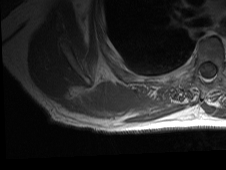
MRI of an extremity soft-tissue mass, one axial slice; MR volume resampled by the dataset authors to the PET/CT grid (not the native acquisition matrix); 226 × 170 image matrix, field of view 221 × 166 mm. Male patient. Case-level facts recorded for this patient, not image findings: histological type: pleiomorphic spindle cell undifferentiated; grade: high; site of the primary tumour: right parascapusular.
Structures marked on this image (expert contour drawn on MRI and transferred to this co-registered scan by the dataset authors):
- gross tumour volume including surrounding oedema: bounding box [x1, y1, x2, y2] px = [58, 81, 187, 123]
- gross tumour volume (mass): [89, 84, 123, 107]